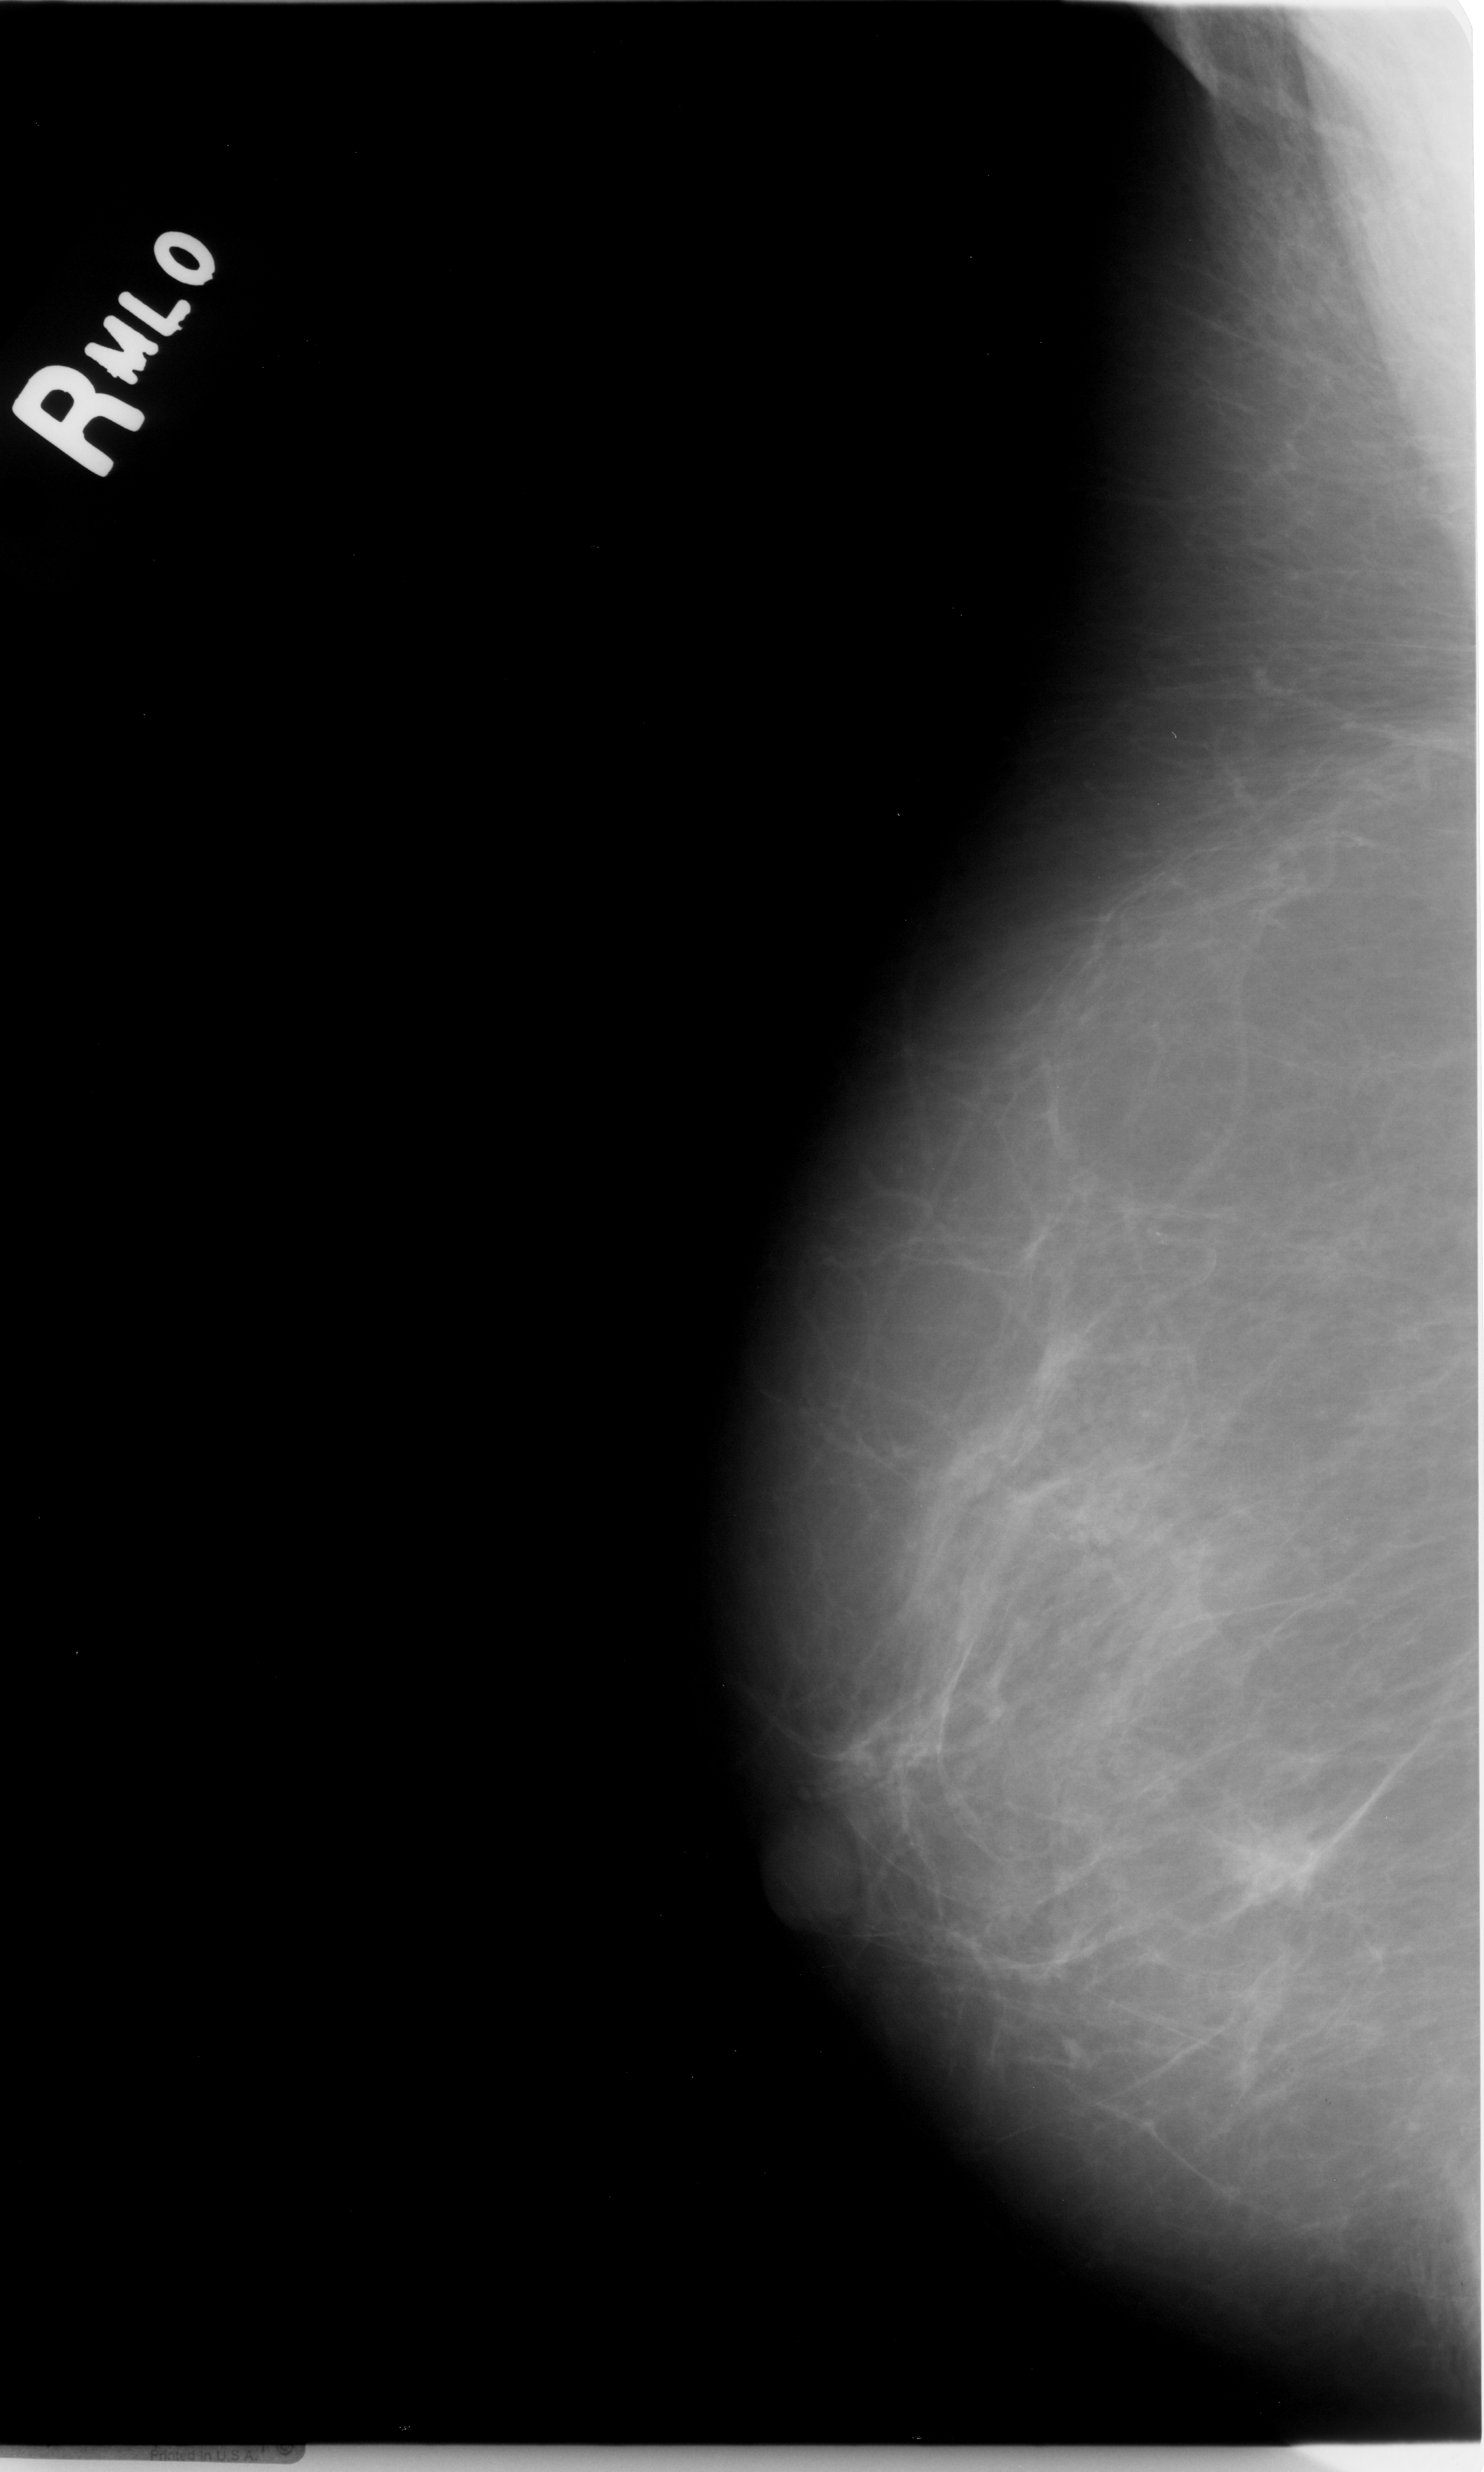
Scanned film-screen mammogram; right breast; MLO view; 1484 × 2472 image matrix.
Expert-marked regions of interest on this image (one box per marked abnormality):
- mass, shape irregular, margins microlobulated; BI-RADS assessment category 5; pathology result (as recorded, not read from the image): malignant: bounding box <1183,1787,1334,1931> (left, top, right, bottom; pixels)